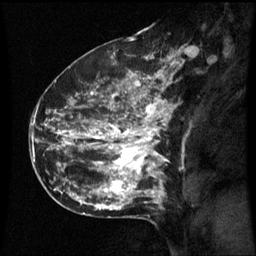
Breast MRI (dynamic contrast-enhanced), one sagittal slice; position 40 of 60 along the scan axis; dynamic contrast-enhanced series, image 2 of 3 at this slice position (ordered by acquisition); 1.5 T; TE 4.2 ms, TR 8.9 ms; 2.1 mm slice thickness; 256 × 256 image matrix, field of view 200 × 200 mm. Female patient, age 42 years. Case-level facts recorded for this patient, not image findings: setting: breast cancer imaged before/during neoadjuvant chemotherapy; receptor status: HER2-positive.
Annotated regions visible in this slice (semi-automatic segmentation, software-assisted and operator-edited):
- analysis volume of interest (the breast-tissue region the enhancement analysis was run in; not a lesion): box from (x=66, y=82) to (x=173, y=193) px
- tumour enhancement mask (voxels above the 70 % enhancement threshold inside the analysis volume of interest): (x=66, y=82)–(x=167, y=193)